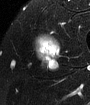
MRI of an extremity soft-tissue mass, one axial slice. Position 48 of 65 along the scan axis. T2-weighted fat-saturated. MR volume resampled by the dataset authors to the PET/CT grid (not the native acquisition matrix). 3.27 mm slice thickness. 90 × 105 image matrix, field of view 88 × 103 mm. Male patient. From the clinical record (not read from this slice): histological type: mixoid liposarcoma; grade: low; site of the primary tumour: left thigh.
Structures marked on this image (expert contour drawn on MRI and transferred to this co-registered scan by the dataset authors):
- gross tumour volume (mass): bounding box [x1, y1, x2, y2] px = [36, 40, 58, 61]